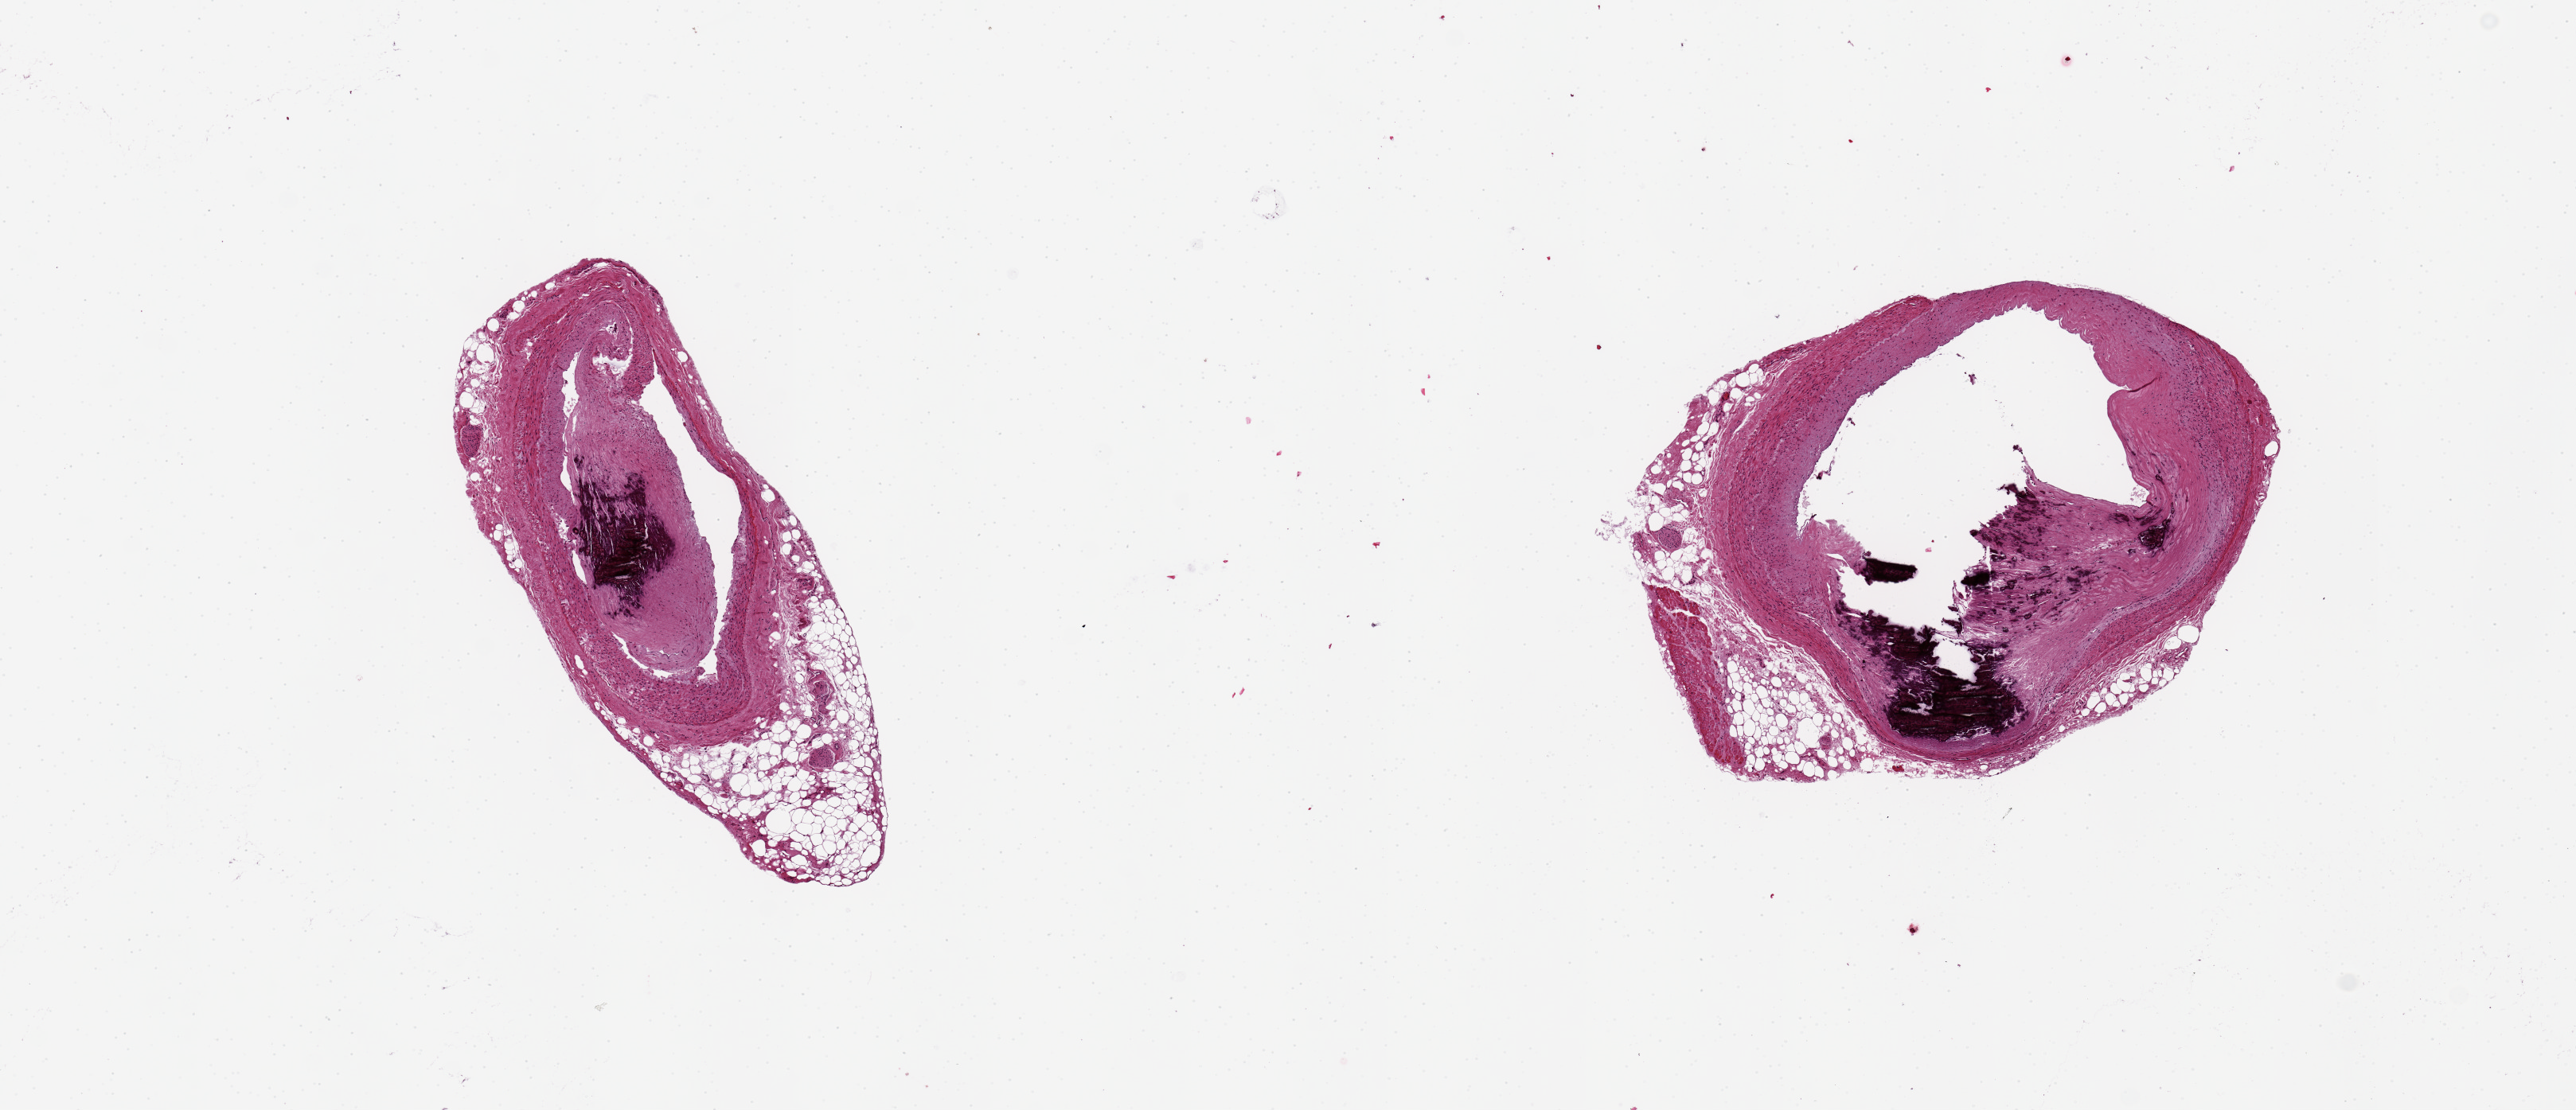
Whole-slide image, hematoxylin and eosin (H&E) stain, brightfield — low-resolution overview of the scanned area, about 12.8 x 5.5 mm (from a 20x scan), PAXgene-fixed, paraffin-embedded tissue, section of coronary artery (target tissue), donor tissue sample. Male donor.
Review note (as recorded): 2 arteries up to 2.8 mm; with calcified plaques and >50% occlusion.